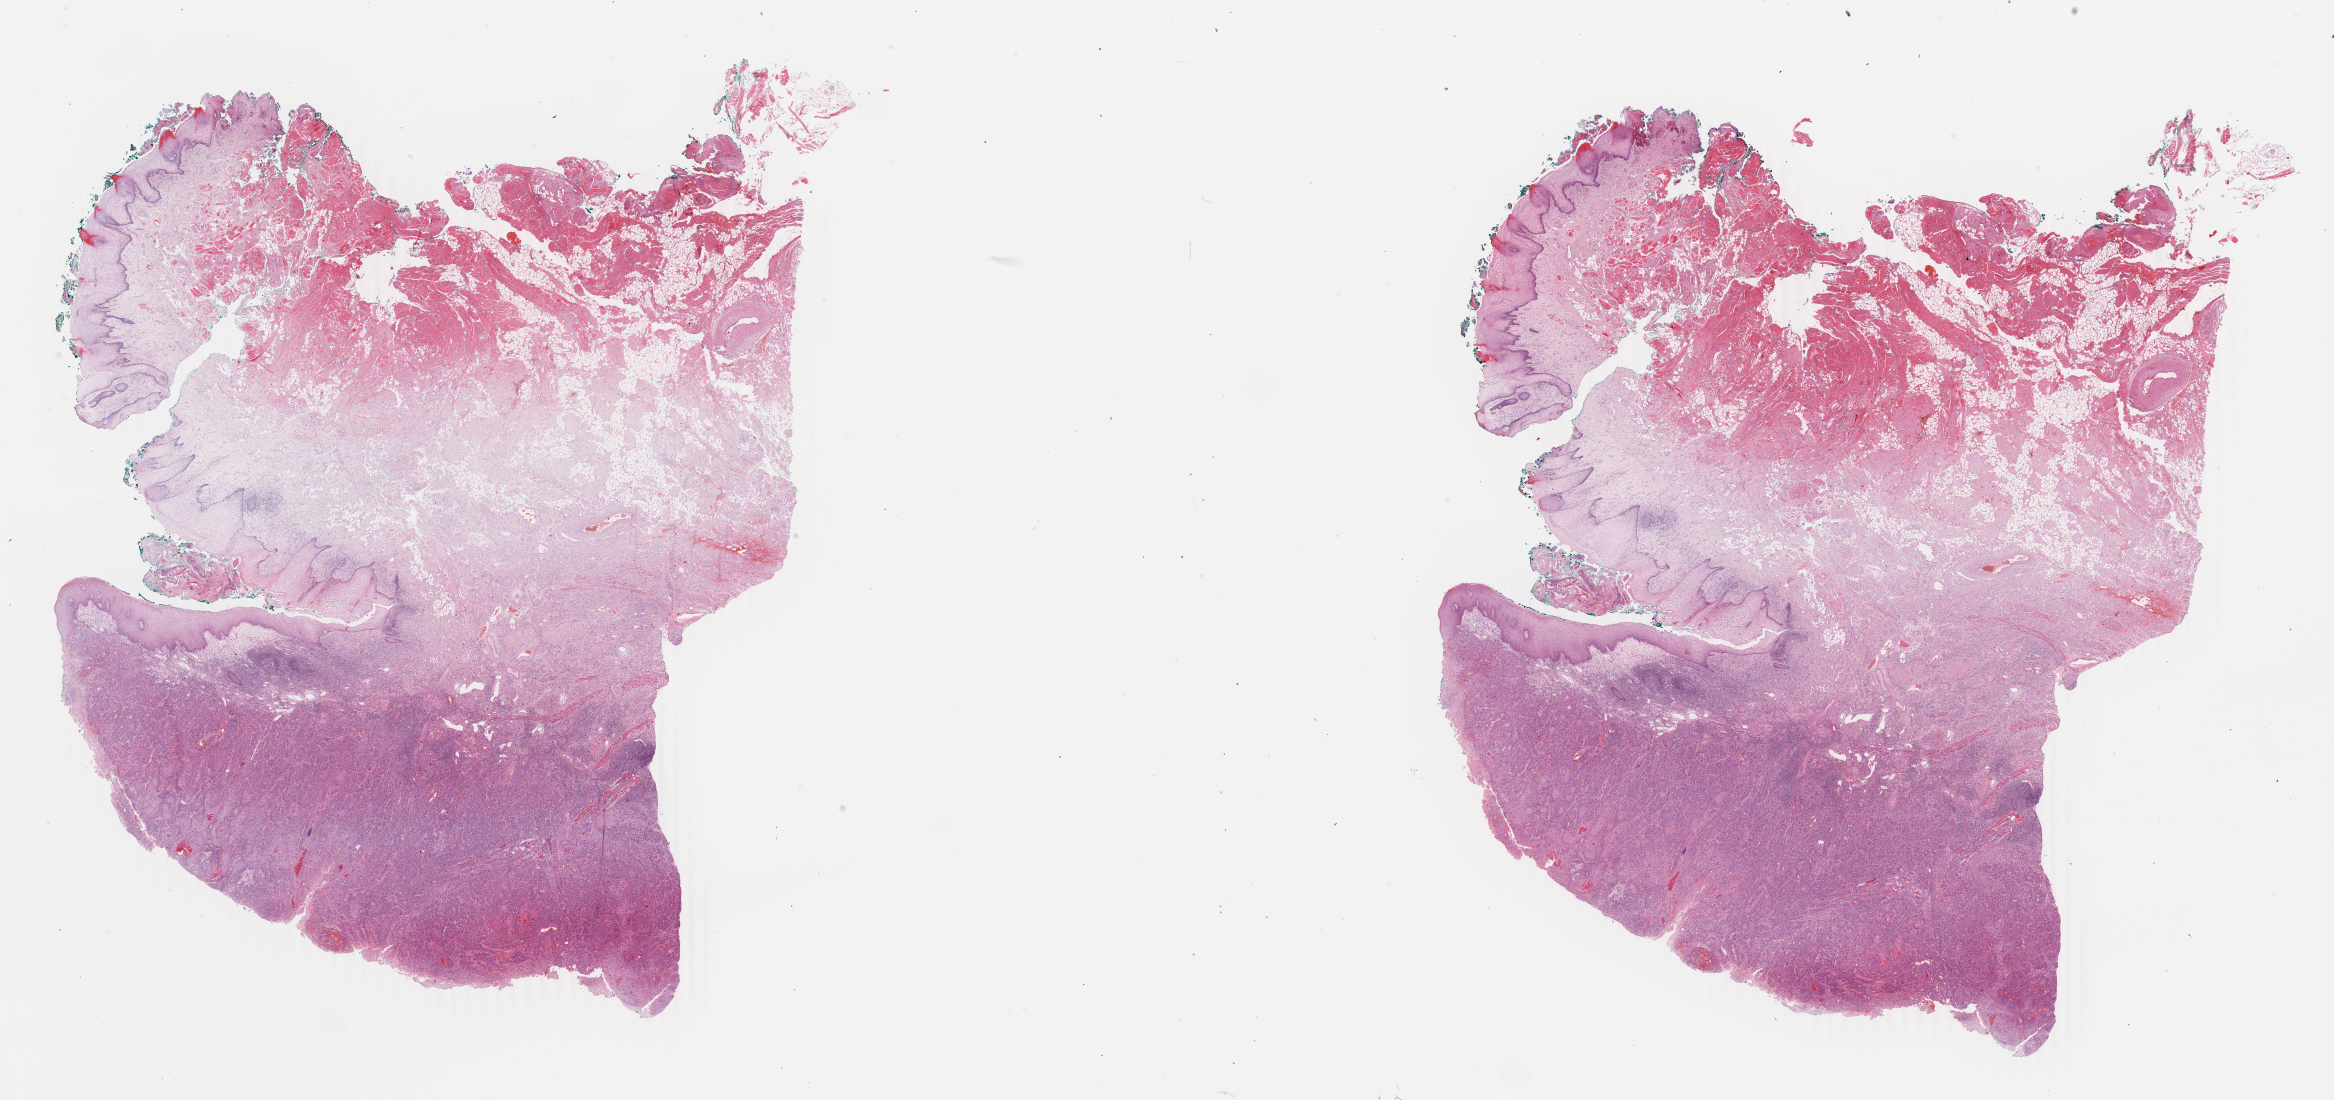
Whole-slide histology image, H&E — shown as a low-resolution overview of the whole scanned area (about 37.1 x 17.5 mm), formalin-fixed paraffin-embedded (FFPE) diagnostic section, primary tumour sample from the head and neck. Patient: male, age at initial diagnosis 59 years. Histologic grade: G2 (moderately differentiated).
AJCC pathologic stage: IVA (7th edition). Pathologic diagnosis: Squamous cell carcinoma, keratinizing, NOS.